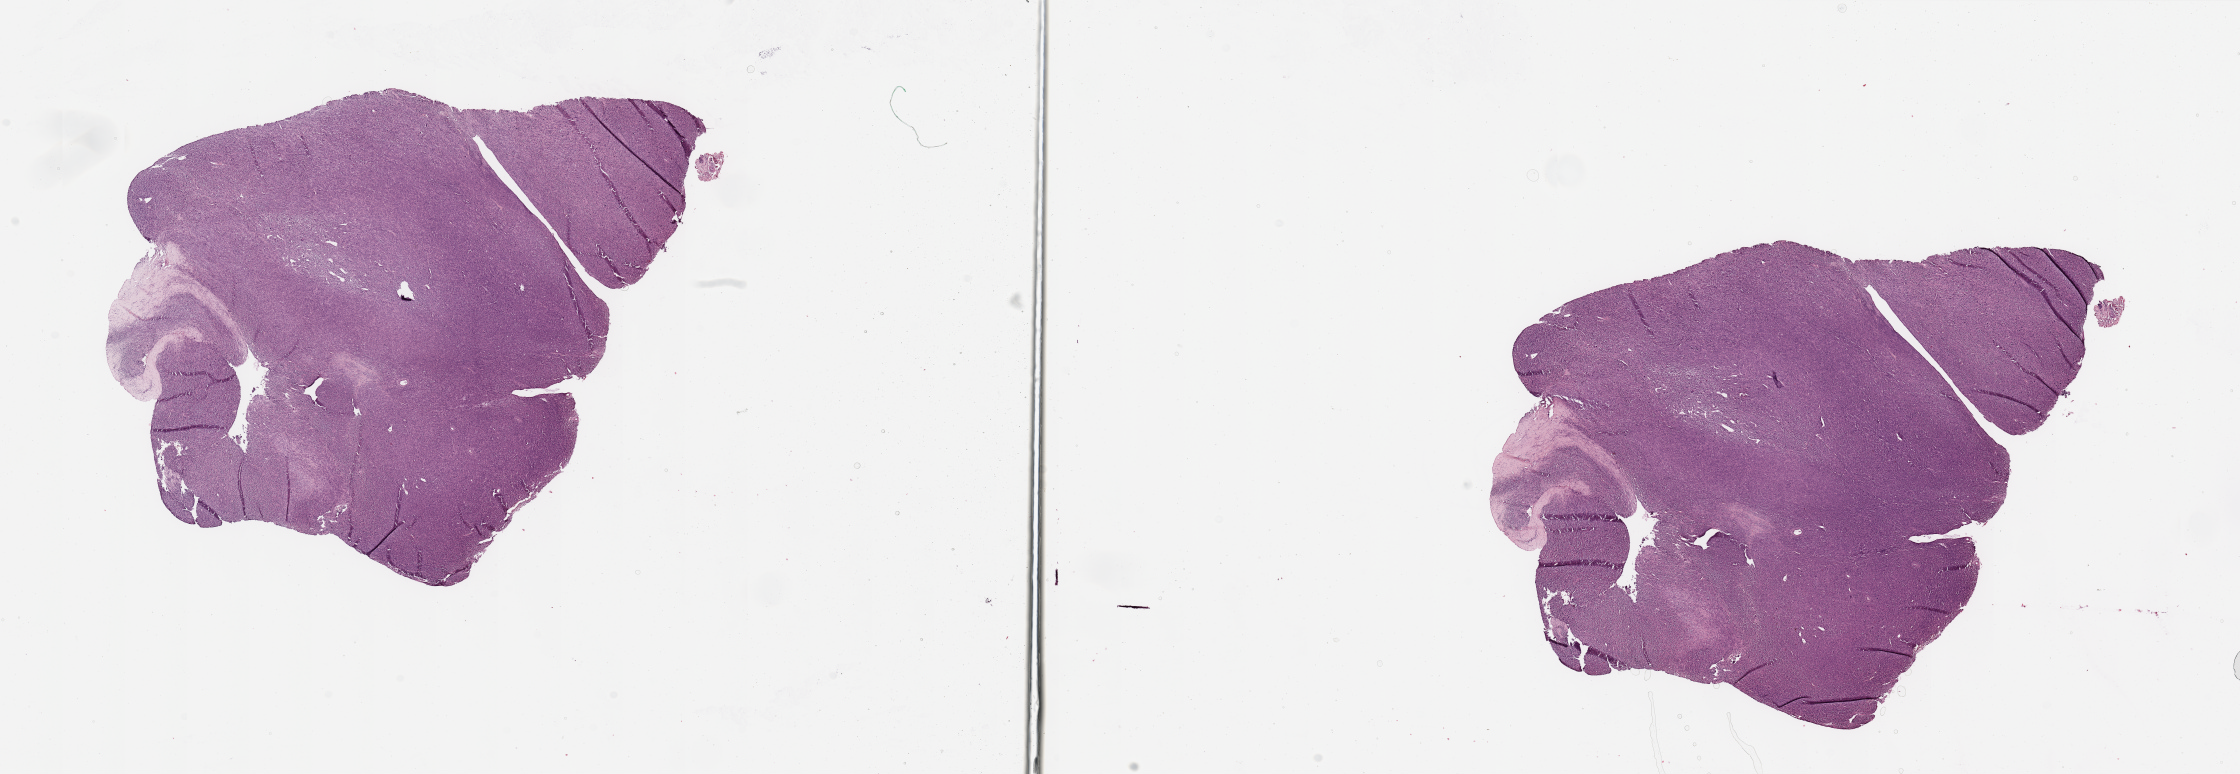
Digitized H&E-stained tissue section (whole slide) — a low-resolution overview of the entire scanned area, about 35.4 x 12.2 mm; tumour tissue sample. 52-year-old female patient.
* patient diagnosis (cohort enrolment): sarcoma (site not recorded at cohort level)
* primary tumour site (as recorded): lower extremity